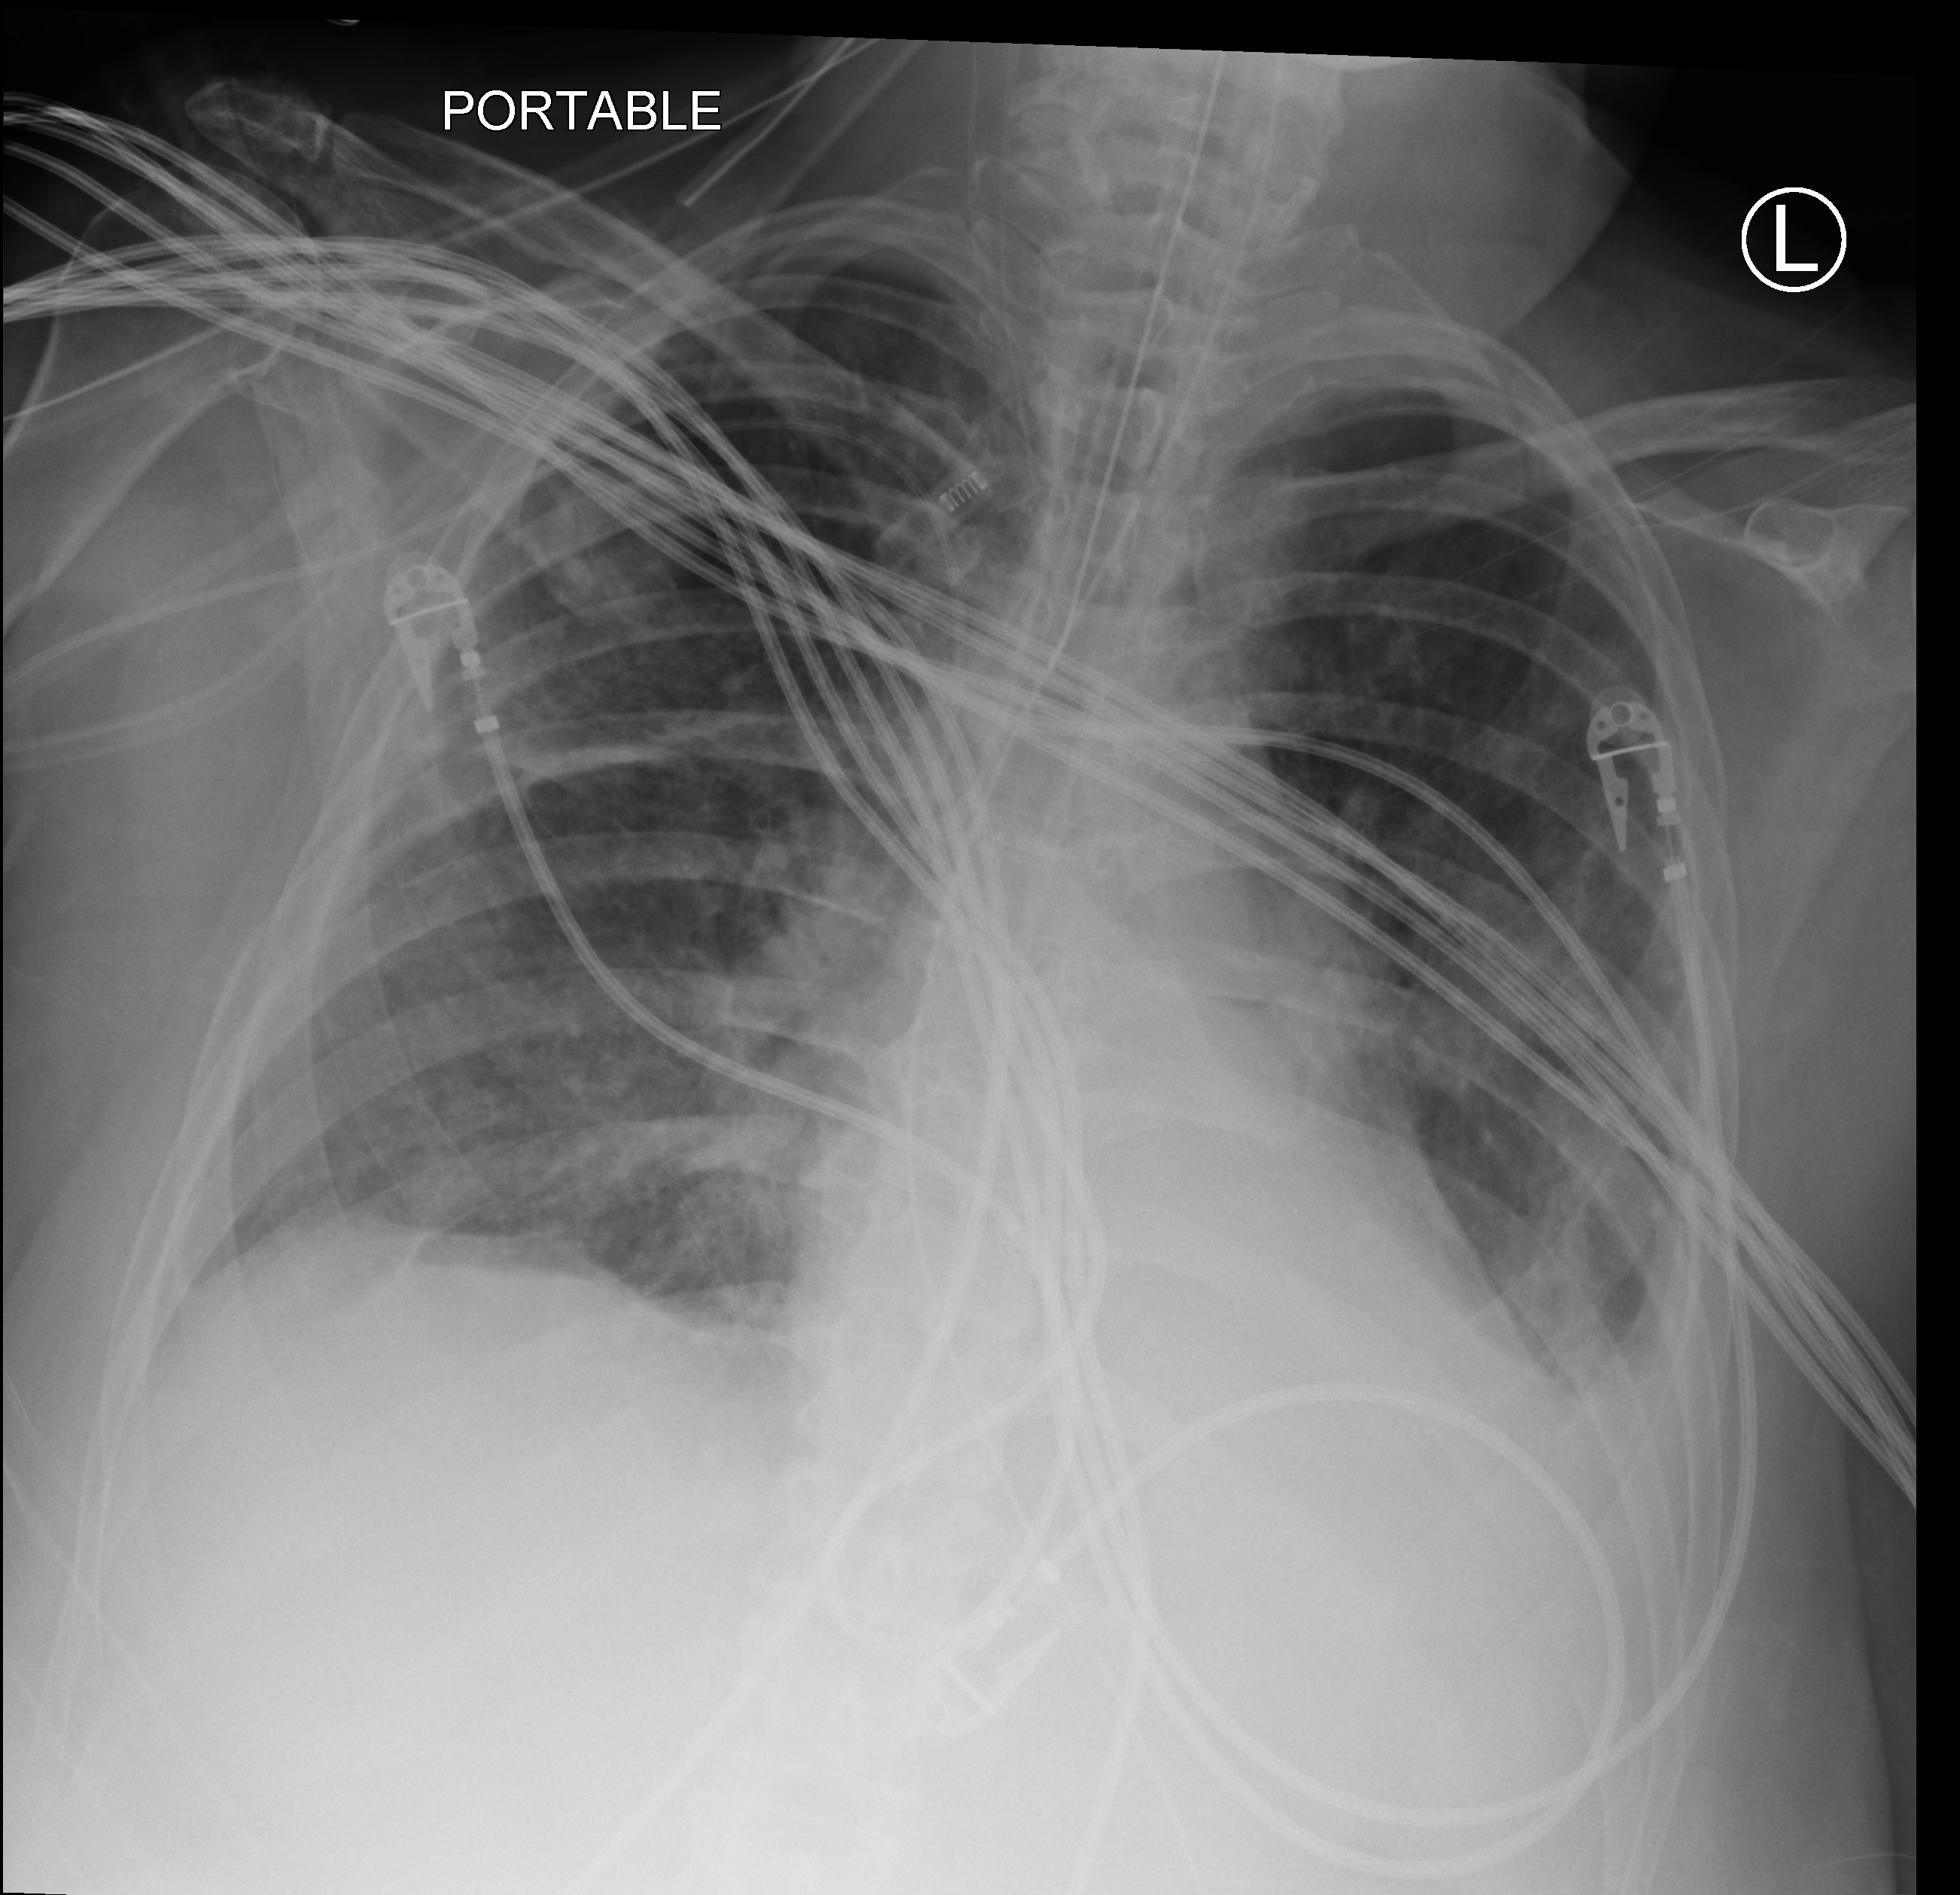
Bedside chest radiograph (computed radiography); anteroposterior (AP) projection. Patient hospitalised with COVID-19; female, aged 60–74 years.
From the hospital-stay record, not from the radiograph (when in the stay this image was taken is not recorded):
- mechanically ventilated during this hospital stay: yes
- admitted to intensive care during this hospital stay: yes